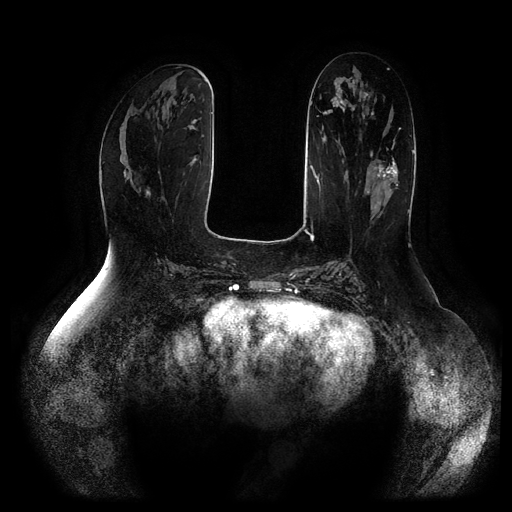
Breast MRI (dynamic contrast-enhanced, multi-phase), one axial slice; slice 39 of 116 in the series (ordered by position); dynamic contrast-enhanced series, time point 2 of 5 at this slice position (early post-contrast); 1.5 T; TE 2.5 ms, TR 5.2 ms; 512 × 512 image matrix, field of view 400 × 400 mm. Female patient, age 66 years.
Structures marked on this image (semi-automatic segmentation, software-assisted and operator-edited):
- breast lesion (labelled 'tumour' in the annotation; benign lesions carry a separate 'benign' label): bounding box [x1, y1, x2, y2] px = [374, 158, 399, 191]